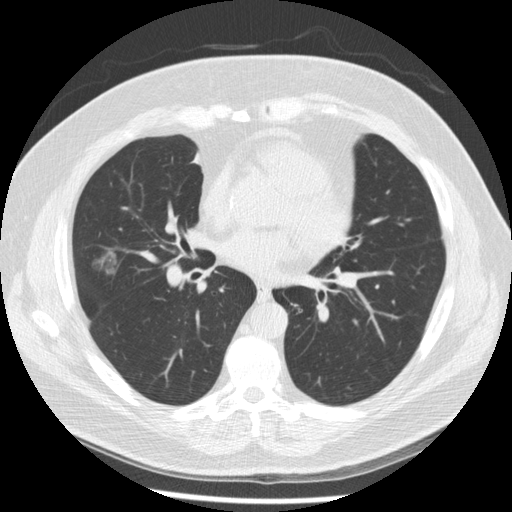
Low-dose screening chest CT, one axial slice; position 111 of 230 along the scan axis; 120 kVp; lung window (W 1500 / L -600 HU); 2.5 mm slice thickness; 512 × 512 image matrix, field of view 360 × 360 mm.
Outlined on this slice (manually delineated by an expert):
- lesion 1 (tumor, middle lobe of right lung): bounding box (x1, y1, x2, y2) in pixels: (93, 251, 120, 276)